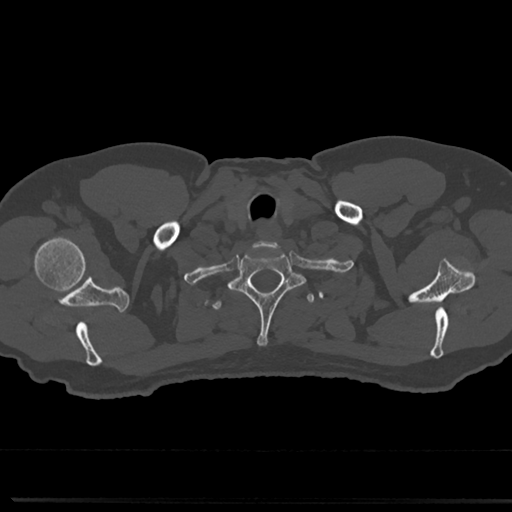
CT including the spine, one axial slice. Slice 672 of 817 in the series (ordered by position). Reconstruction kernel Br40s/3. 120 kVp. Bone window (W 1800 / L 400 HU). 512 × 512 image matrix, field of view 355 × 355 mm. Male patient, age 61 years. Case-level facts recorded for this patient, not image findings: primary cancer: prostate.
Outlined on this slice (semi-automatically segmented with operator editing):
- T1 vertebra: bounding box <232,248,299,346> (left, top, right, bottom; pixels)
- T2 vertebra: <212,291,315,314>